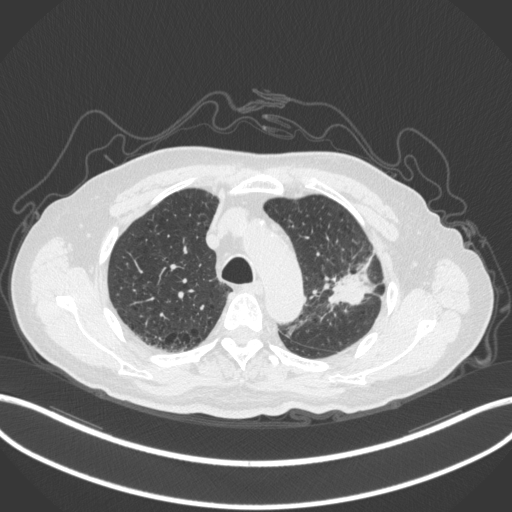
Chest CT, one axial slice; slice 225 of 331 in the series (ordered by position); reconstruction kernel B31f; 120 kVp; lung window (W 1500 / L -600 HU); 1 mm slice thickness; 512 × 512 image matrix, field of view 400 × 400 mm. Patient: male, 79 years. Case-level facts recorded for this patient, not image findings: clinical TNM (as recorded): T2a N1 M1; histopathological grade: G3.
Outlined on this slice (bounding box drawn by a radiologist):
- lung tumour (recorded histology: adenocarcinoma): bounding box (x1, y1, x2, y2) in pixels: (325, 244, 383, 307)